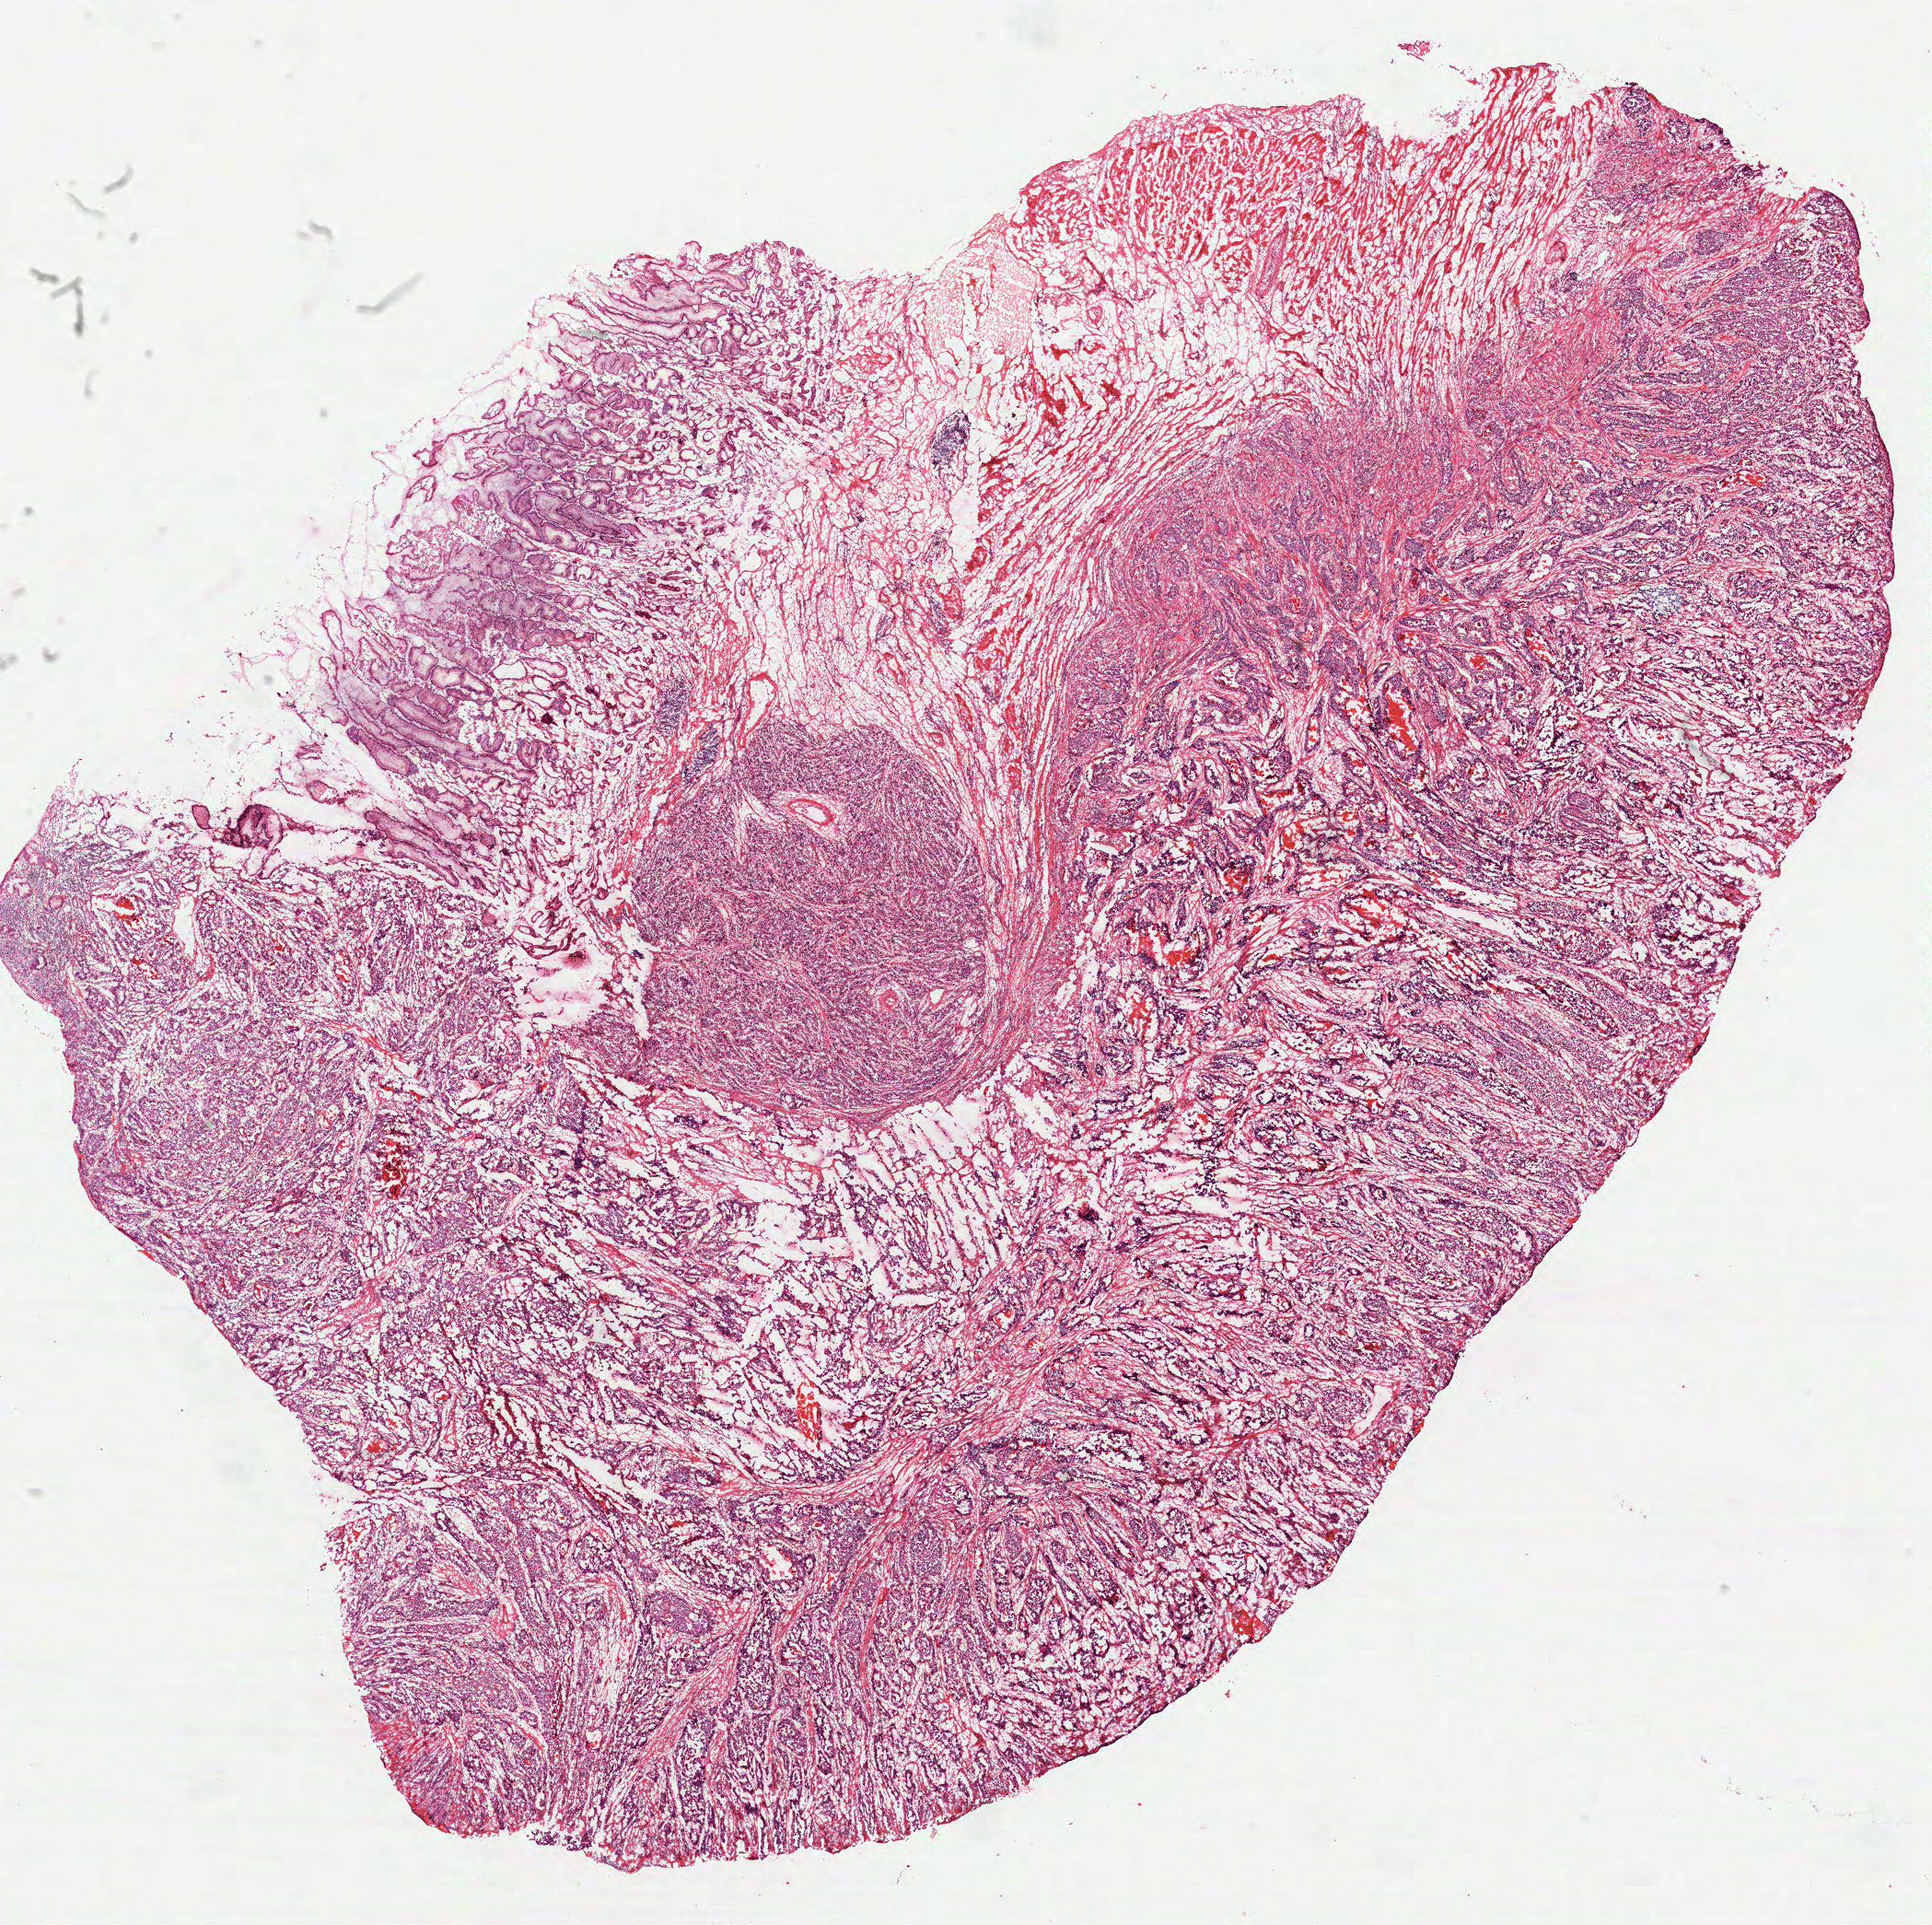
H&E whole-slide image — shown as a low-resolution overview of the whole scanned area (about 16.9 x 16.9 mm), frozen section, stomach, primary tumour sample. Patient: female, age at initial diagnosis 68 years. Histologic grade: G3 (poorly differentiated). Pathologist review of this section (percent, as recorded): tumour cells 70%, tumour nuclei 75%, normal cells 12%, stromal cells 15%, necrosis 3%. Infiltration values recorded for this section: lymphocyte infiltration 15%.
Lymph nodes positive (case pathology): 7 of 13 examined. AJCC pathologic stage: IIIC (7th edition). TNM: T4 N3a M0. Diagnosis: Adenocarcinoma, NOS.